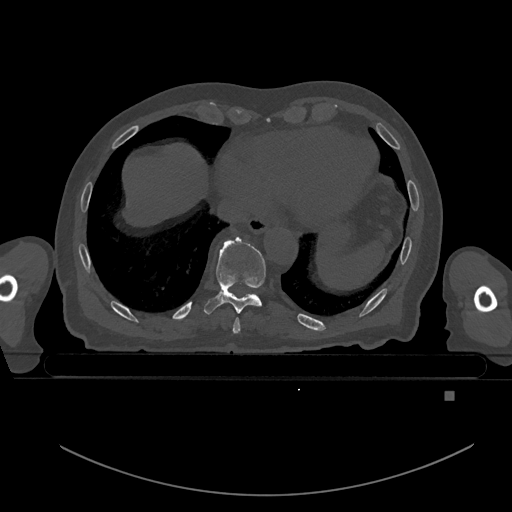
CT including the spine, one axial slice; bone window (W 1800 / L 400 HU); 0.5 mm slice thickness; 512 × 512 image matrix, field of view 456 × 456 mm. Patient: male, 82 years. Case-level facts recorded for this patient, not image findings: primary cancer: prostate.
Outlined on this slice (semi-automatically segmented with operator editing):
- T8 vertebra: bounding box [x1, y1, x2, y2] px = [233, 318, 240, 334]
- T9 vertebra: [204, 237, 266, 314]